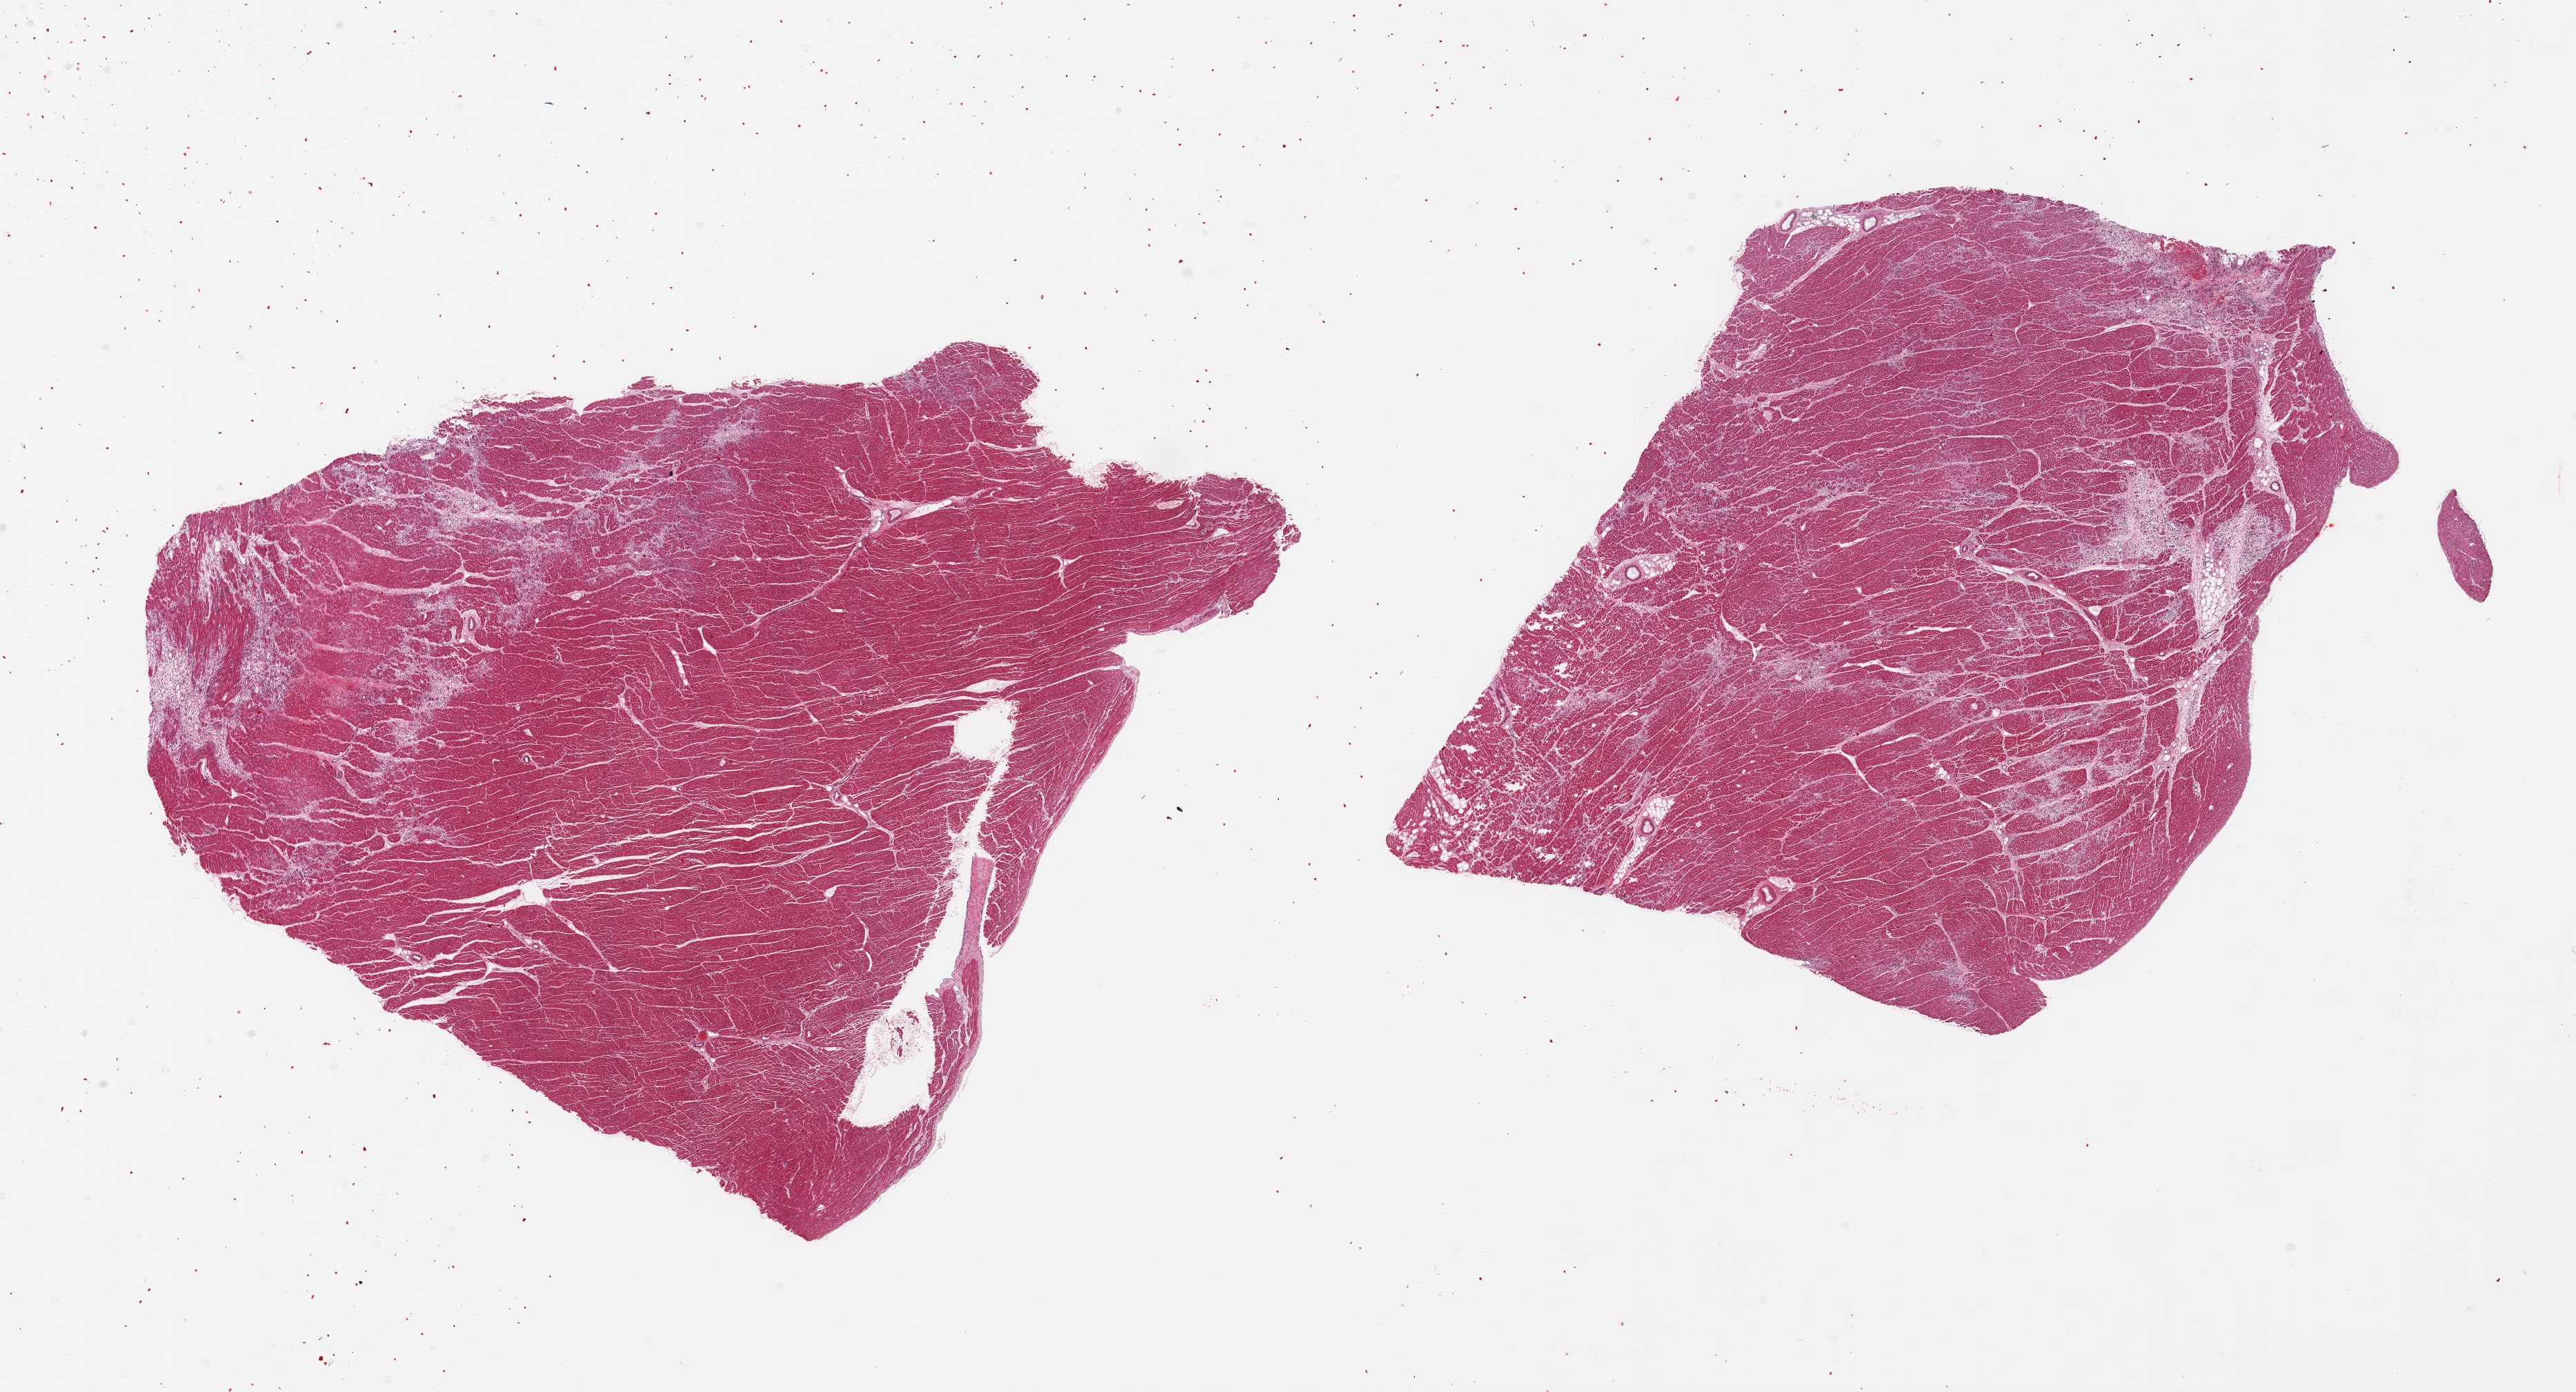
Digitized hematoxylin and eosin (H&E)-stained section, whole scanned area (about 29.5 x 16.0 mm, from a 20x scan) shown as a low-resolution overview; PAXgene-fixed, paraffin-embedded tissue; target tissue: heart; tissue donor sample. Donor: male.
Pathologist's review note for this sample: 2 pieces; multiple patchy areas of necrosis, hemorrhage and granulation tissue with chronic inflammation, c/w recent infarction.